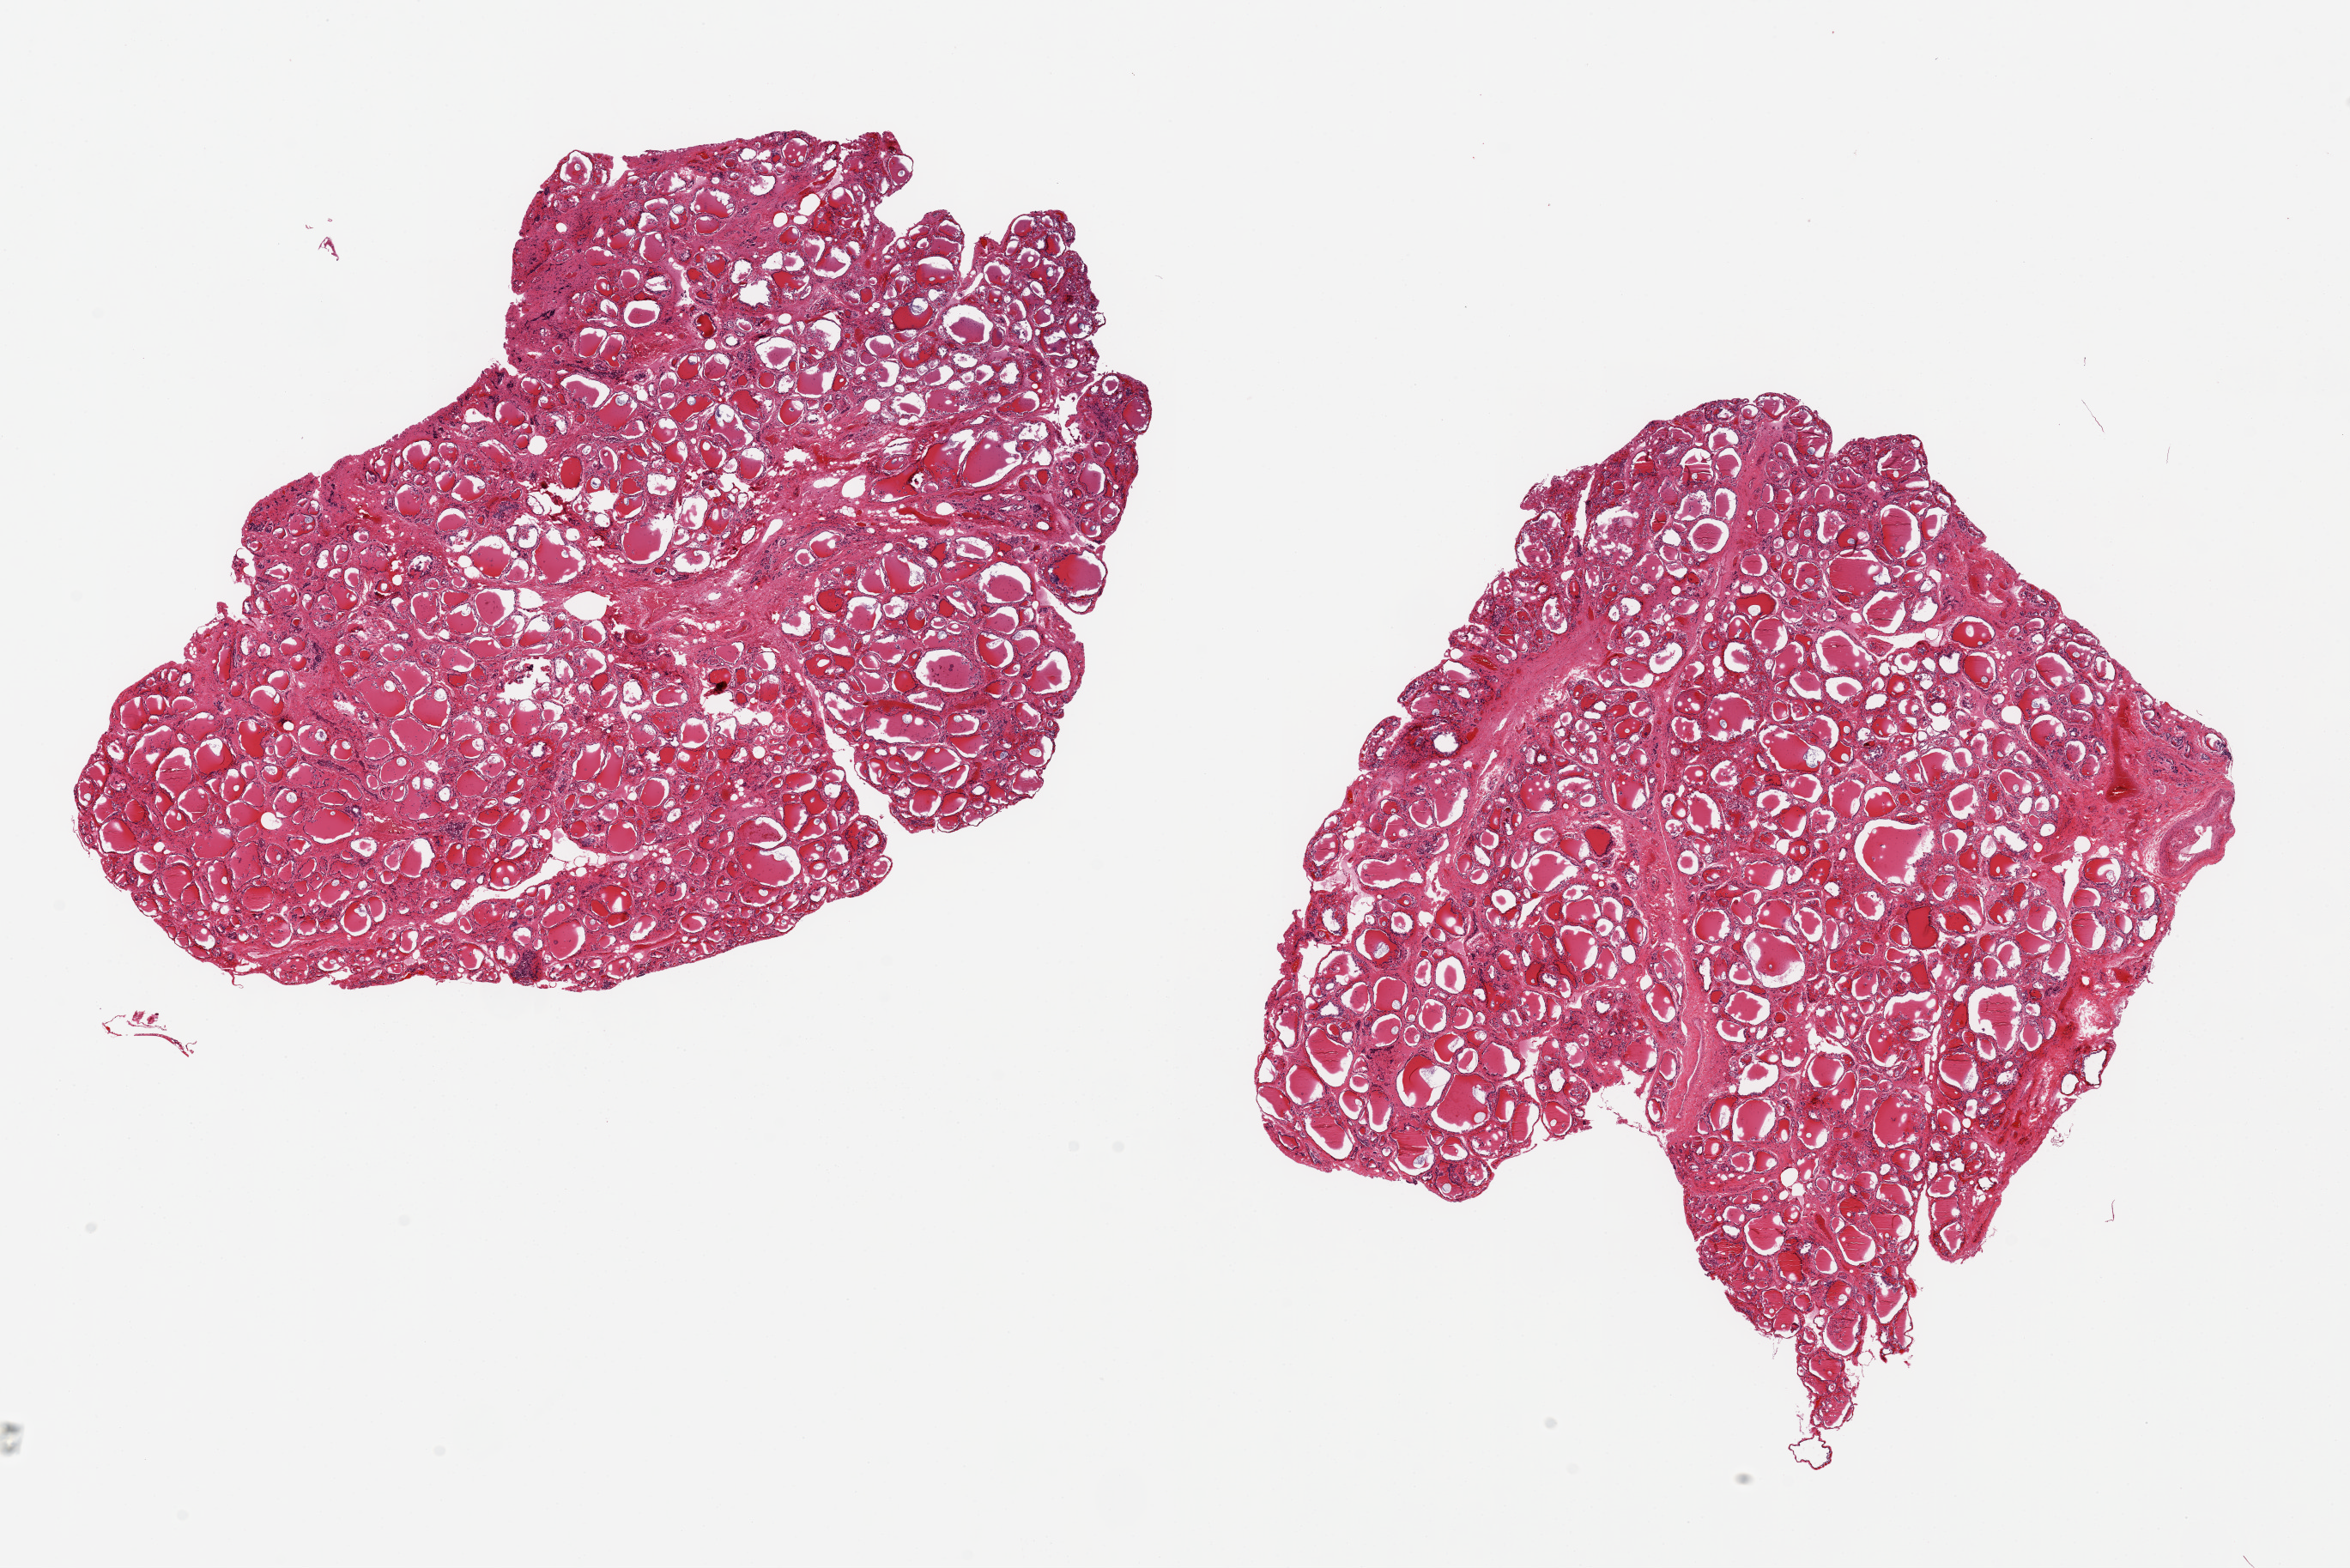
Whole-slide image, H&E stain, brightfield, shown as a low-resolution overview of the whole scanned area (about 21.7 x 14.5 mm); PAXgene-fixed, paraffin-embedded tissue; section of thyroid (target tissue); donor tissue sample. Male donor.
Review note (as recorded): 2 pieces,~8.5 and 10x7mm.